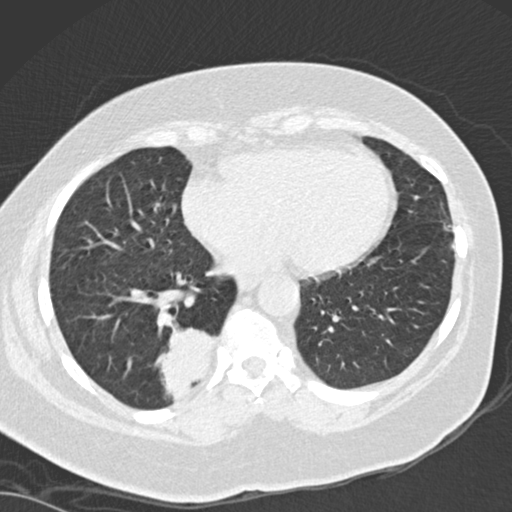
Chest CT (low-dose screening protocol), one axial image; baseline annual screen; lung window (W 1500 / L -600 HU); slice 103 of 162 in the series. Female, age 66 years at enrolment. Current smoker at enrolment.
Lesion marked by an expert reader, bounding box <147,316,232,404> (left, top, right, bottom; pixels). The screening reader recorded 3 non-calcified nodules or masses ≥4 mm on this exam; which of them this box marks is not recorded. Official screen result: positive, change unspecified: nodule(s) >= 4 mm or enlarging nodule(s), mass(es), or other non-specific abnormalities suspicious for lung cancer. Later outcome: lung cancer diagnosed 67 days after this screen — adenocarcinoma, NOS, right lower lobe, well differentiated (G1), stage IB (AJCC 6th edition), 55 mm at pathology.